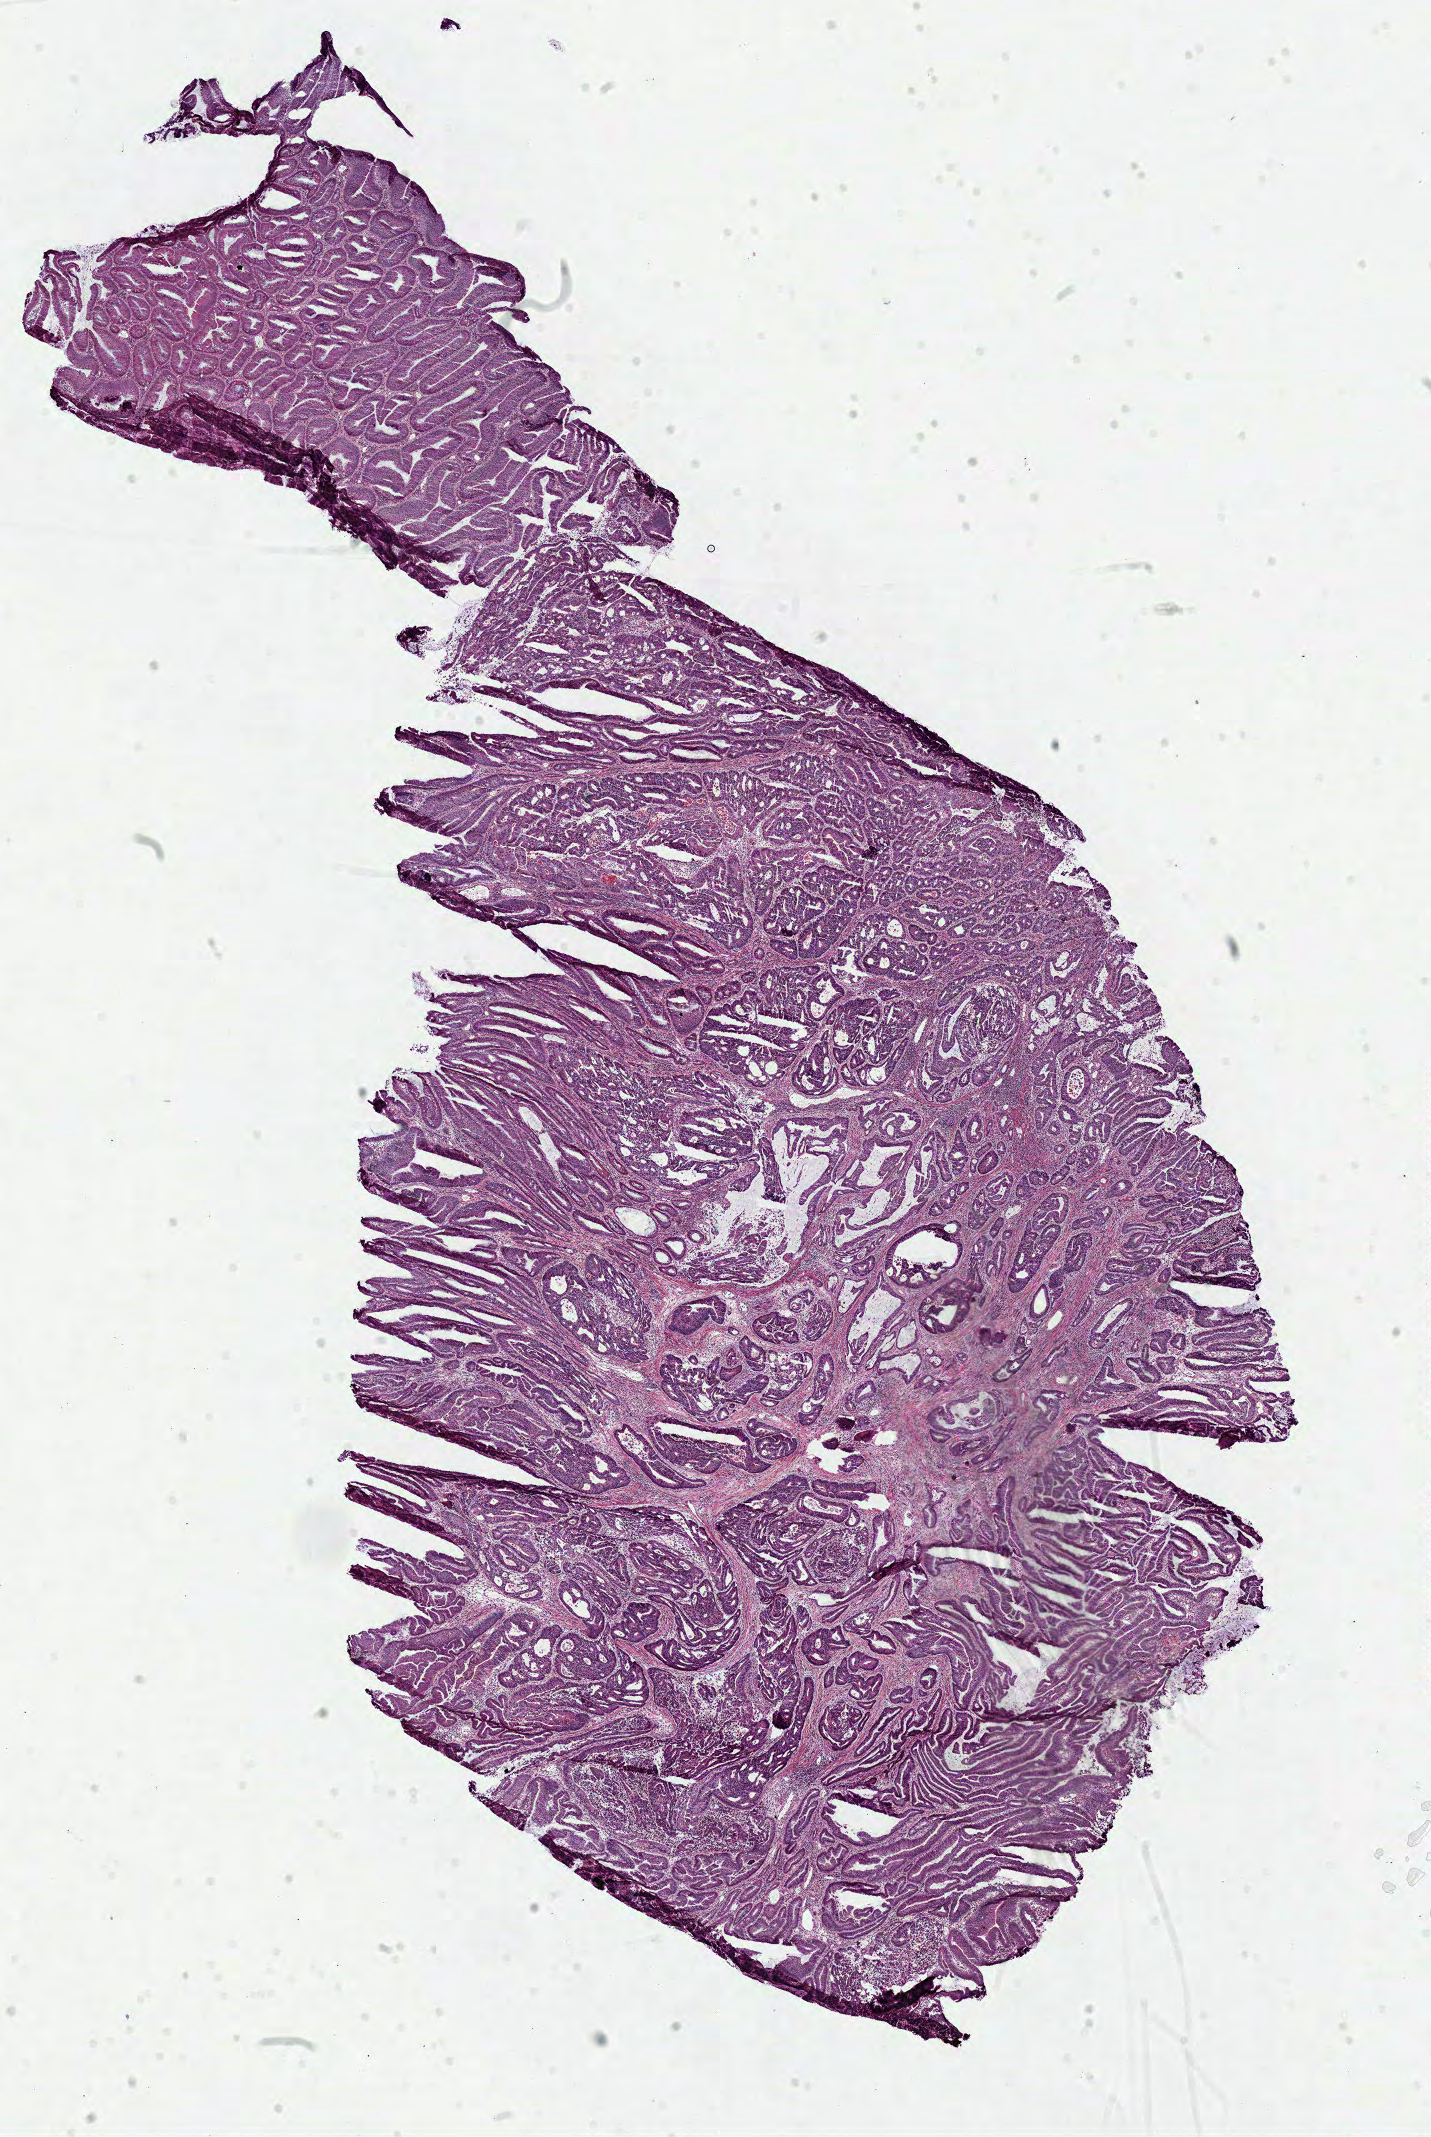
Whole-slide histology image, Hematoxylin and eosin (H&E) stained, low-resolution overview of the scanned area, about 11.3 x 16.8 mm, frozen section from the top of the tissue portion, primary tumour sample from the colon. Patient: male, age at initial diagnosis 73 years. Slide review estimates, as recorded: tumour cells 65%, tumour nuclei 75%, normal cells 15%, stromal cells 10%, necrosis 10%.
Pathologic diagnosis: Adenocarcinoma, NOS (hepatic flexure of colon). AJCC pathologic stage: III (6th edition). Lymph nodes positive (case pathology): 2 of 65 examined.